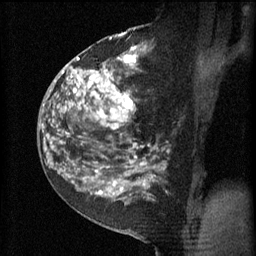
Breast MRI (dynamic contrast-enhanced), one sagittal slice. Position 29 of 60 along the scan axis. 3 images stored at this slice position (order not interpretable as contrast timing). 1.5 T. TE 4.2 ms, TR 11 ms. 2 mm slice thickness. 256 × 256 image matrix, field of view 180 × 180 mm. Female patient, age 52 years.
Structures marked on this image (semi-automatic segmentation, software-assisted and operator-edited):
- analysis volume of interest (the breast-tissue region the enhancement analysis was run in; not a lesion): bounding box [x1, y1, x2, y2] px = [81, 52, 160, 157]
- tumour enhancement mask (voxels above the 70 % enhancement threshold inside the analysis volume of interest): [81, 54, 139, 157]